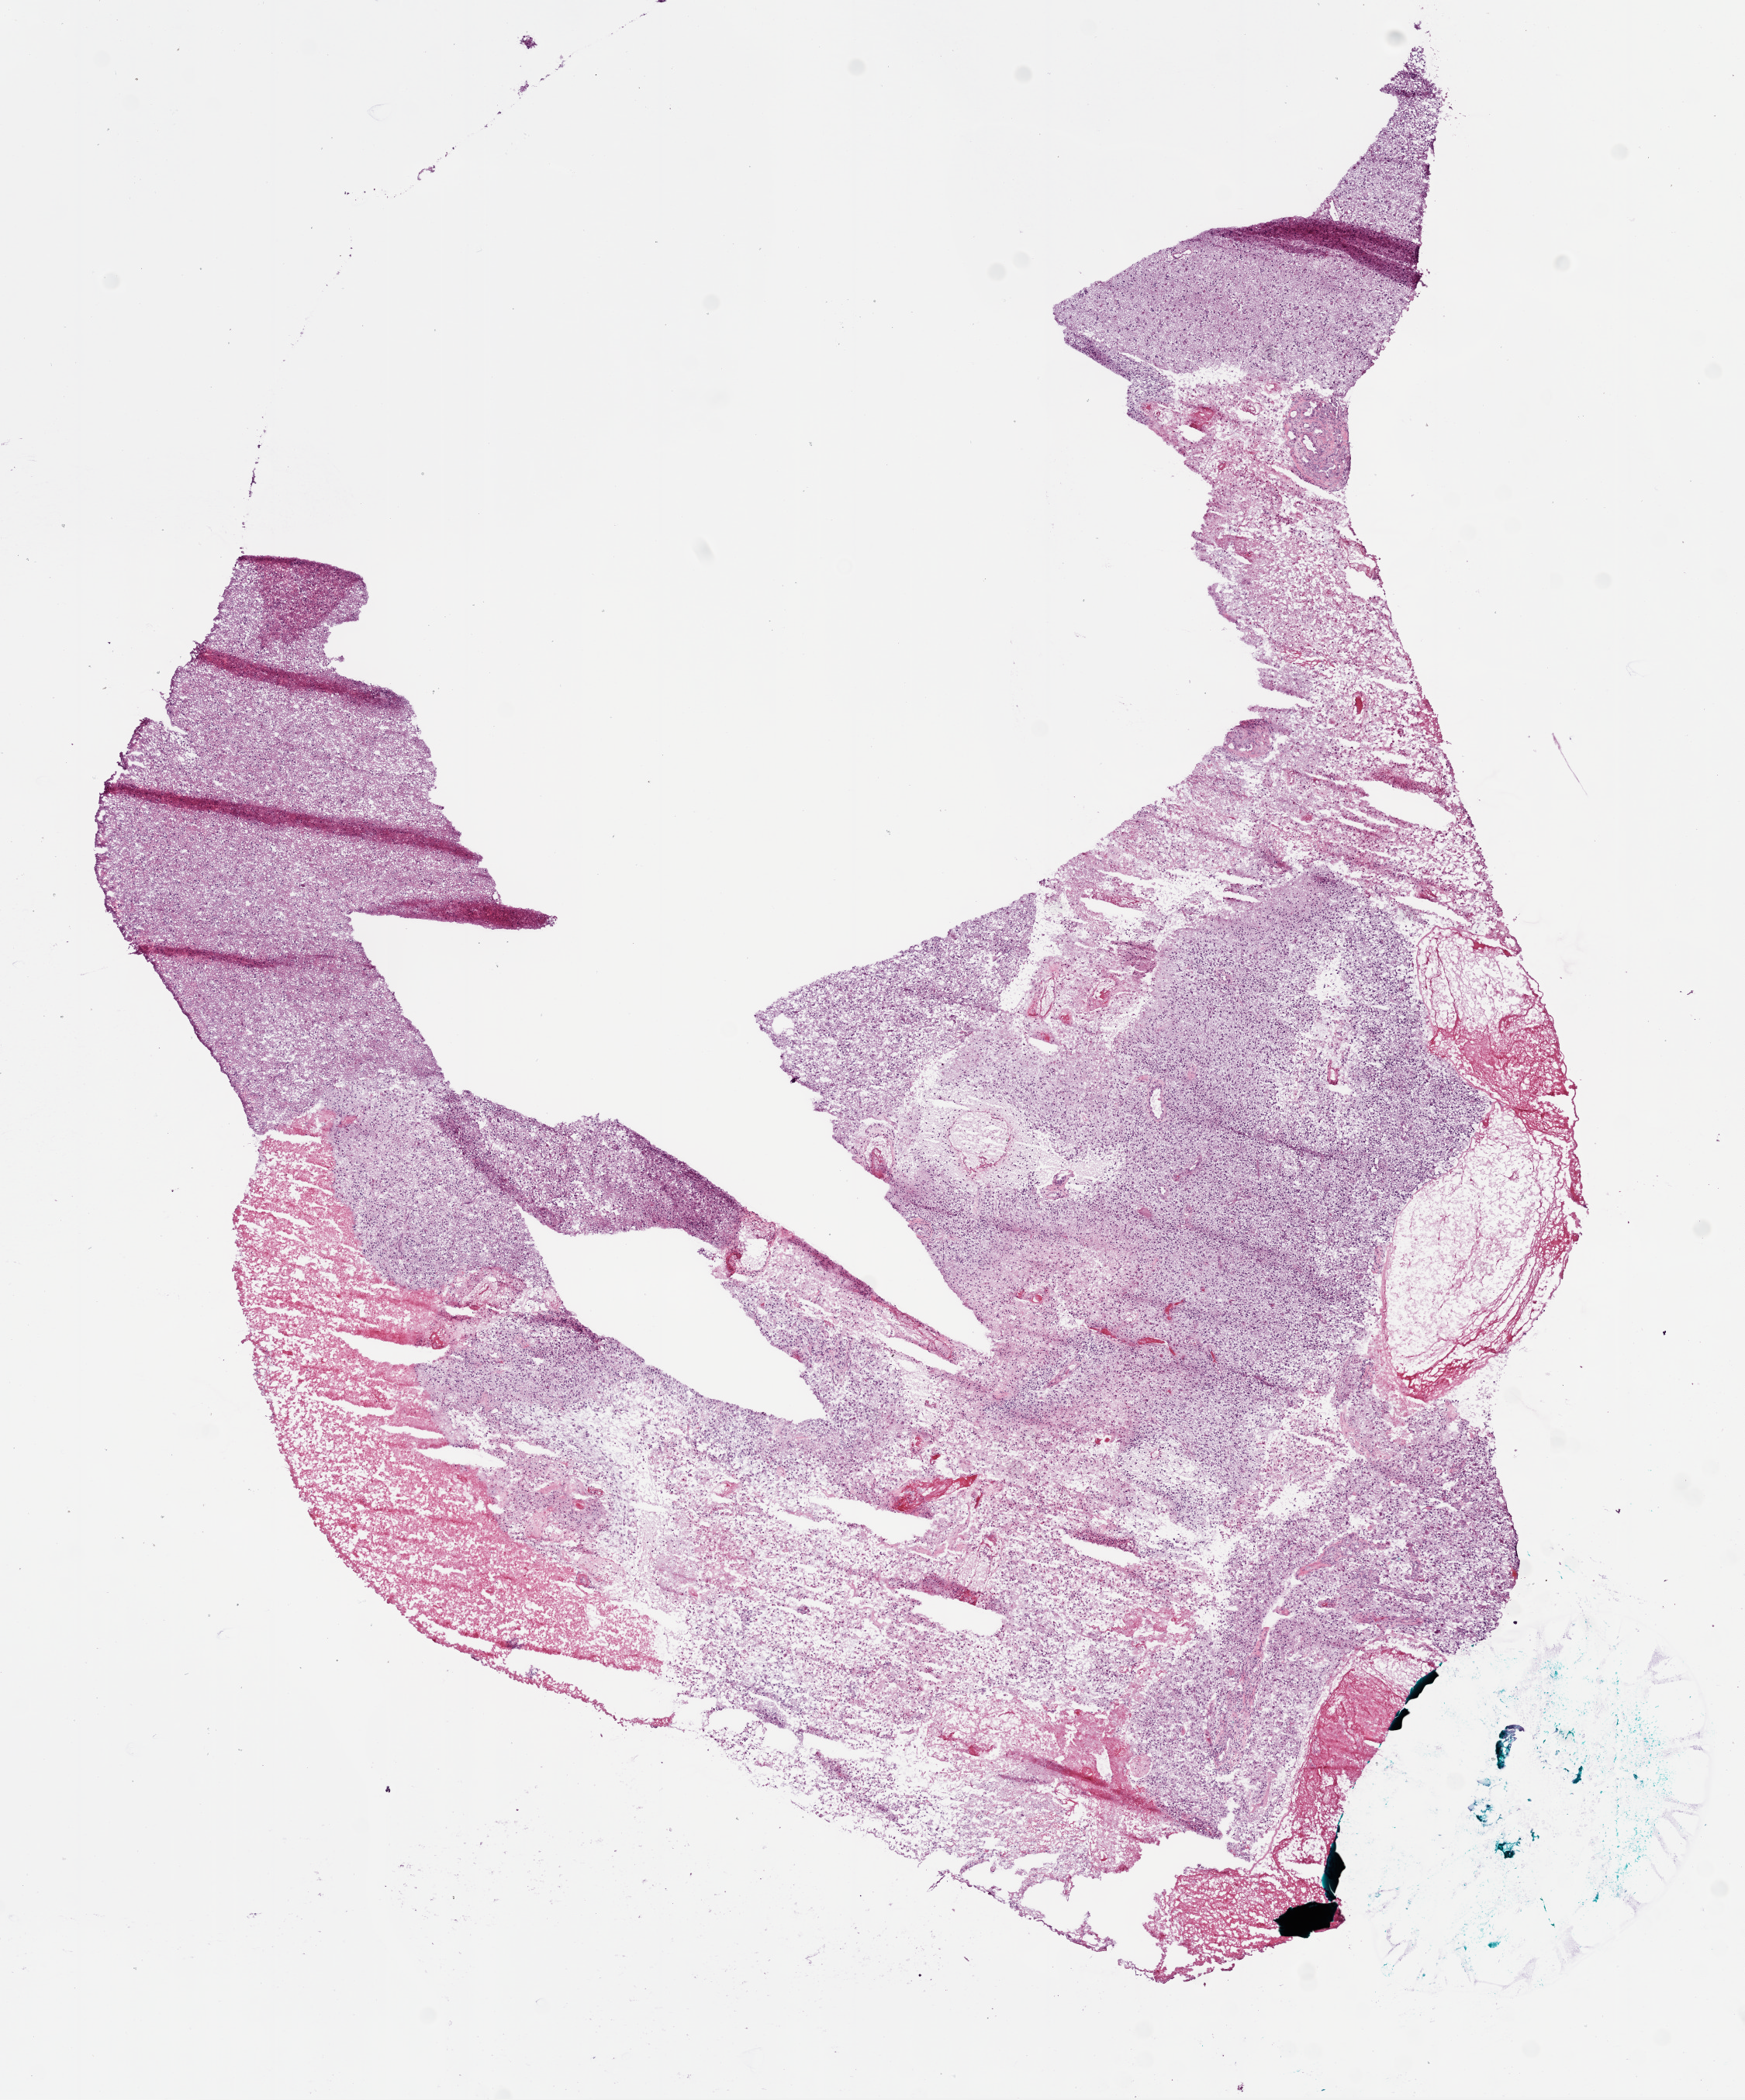
Digitized H&E tissue section (whole slide), a low-resolution overview of the entire scanned area, about 9.0 x 10.9 mm (acquisition: 20x scan); frozen section; sample: primary tumour, brain. Patient: male, age at initial diagnosis 54 years. Slide review estimates, as recorded: tumour cells 65%, tumour nuclei 80%, stromal cells 10%, necrosis 25%.
* pathologic diagnosis: Glioblastoma